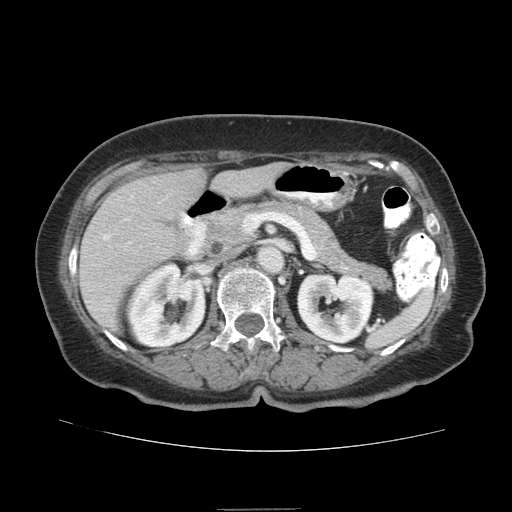
Contrast-enhanced abdominal CT (liver protocol), one axial slice. Slice 37 of 95 in the series (ordered by position). Soft-tissue window (W 400 / L 40 HU). 2.5 mm slice thickness. 512 × 512 image matrix. From the clinical record (not read from this slice): diagnosis: hepatocellular carcinoma (patient treated with transarterial chemoembolisation; whether this scan precedes or follows treatment is not stated here); TNM stage (as recorded): Stage-IVA; Child-Pugh class: B; tumour nodularity: uninodular.
Structures marked on this image (semi-automatic segmentation, software-assisted and operator-edited):
- liver parenchyma outside the tumour (the mass and vessels are separate outlines, so this box may not span the whole liver): box from (x=80, y=162) to (x=286, y=328) px
- liver vessels: (x=103, y=235)–(x=110, y=239)